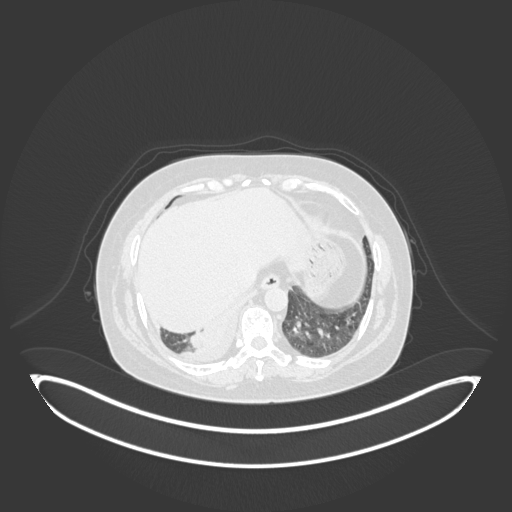
Chest CT, one axial slice. Lung window (W 1500 / L -600 HU). 1 mm slice thickness. 512 × 512 image matrix, field of view 500 × 500 mm. Patient: female, 56 years. From the clinical record (not read from this slice): clinical TNM (as recorded): T2b N1 M0; histopathological grade: G3.
Outlined on this slice (rectangle marked by the reading radiologist):
- lung tumour (recorded histology: small cell carcinoma): box from (x=180, y=321) to (x=212, y=356) px